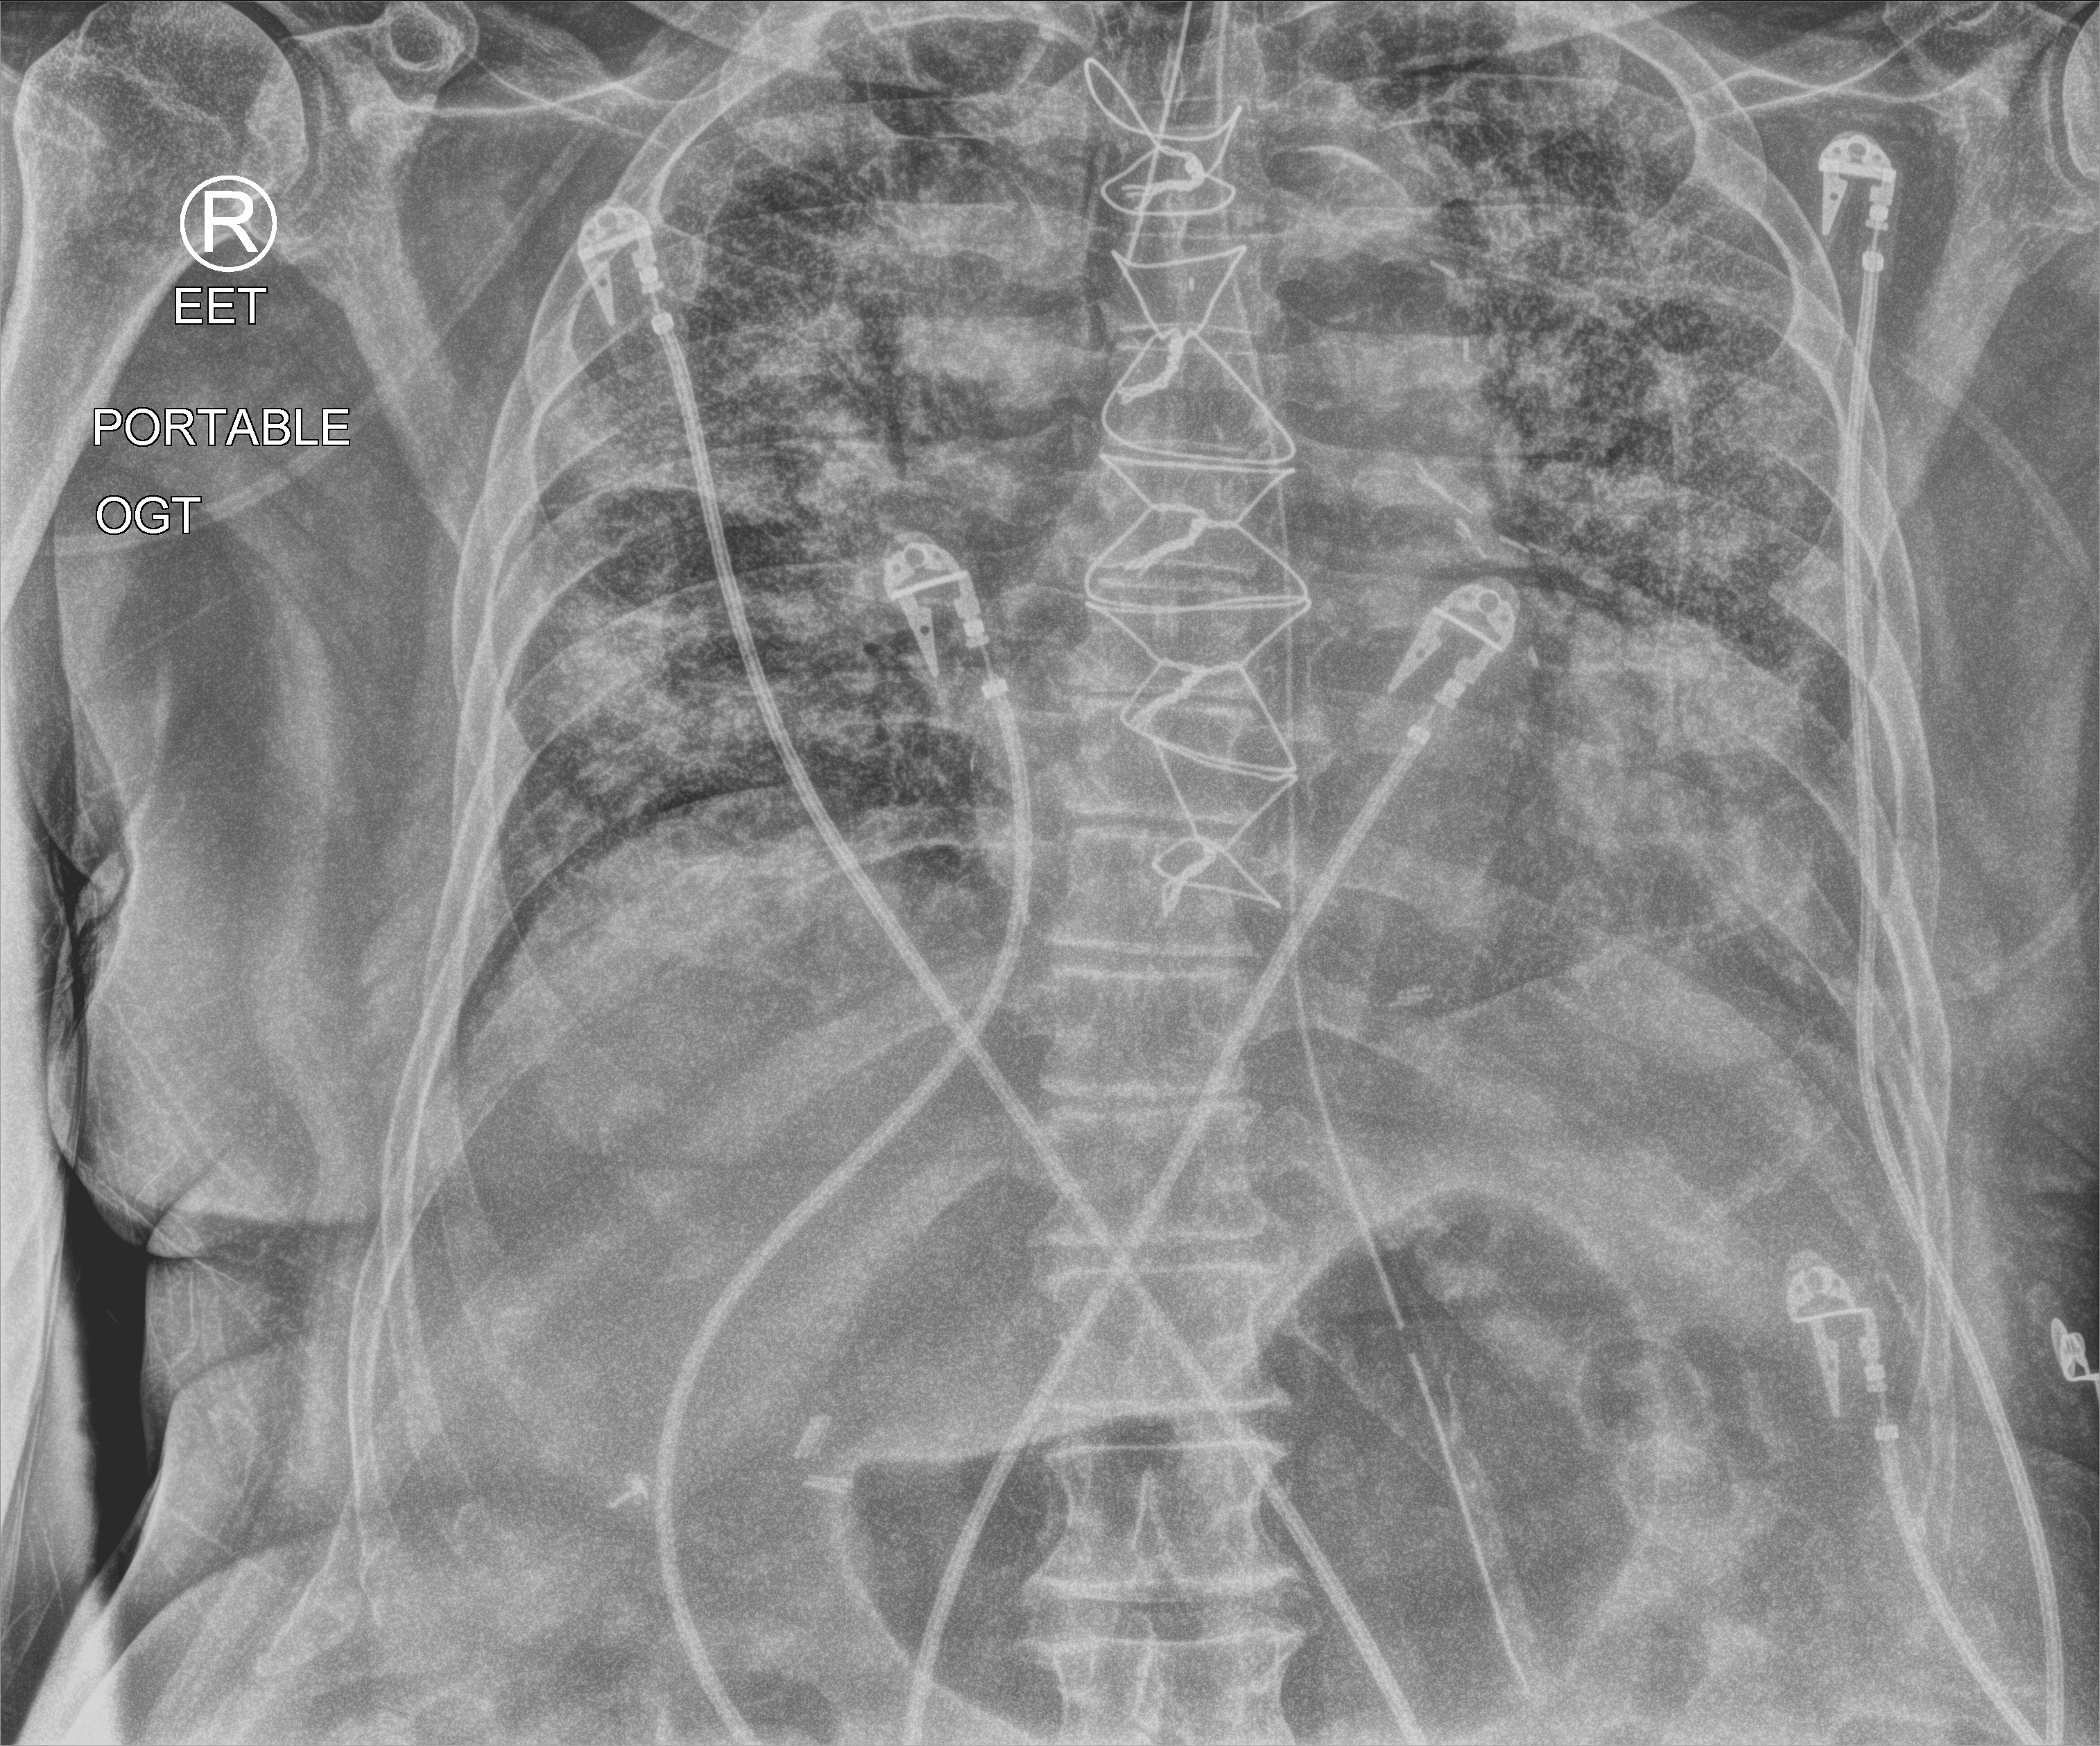
Portable chest radiograph; anteroposterior (AP) projection. Patient hospitalised with COVID-19; male, aged 75–90 years.
Admission-level facts for this patient (not findings on this image; timing relative to this image not recorded): other chronic lung disease (admission record): yes.